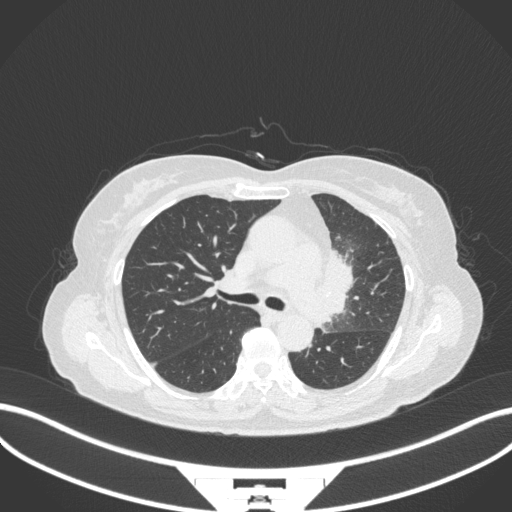
Chest CT, one axial slice. Slice 211 of 382 in the series (ordered by position). Lung window (W 1500 / L -600 HU). 1 mm slice thickness. 512 × 512 image matrix, field of view 400 × 400 mm. Patient: female, 64 years. From the clinical record (not read from this slice): clinical TNM (as recorded): T2a N2 M0.
Outlined on this slice (rectangle marked by the reading radiologist):
- lung tumour (recorded histology: adenocarcinoma): bounding box (x1, y1, x2, y2) in pixels: (319, 243, 358, 330)